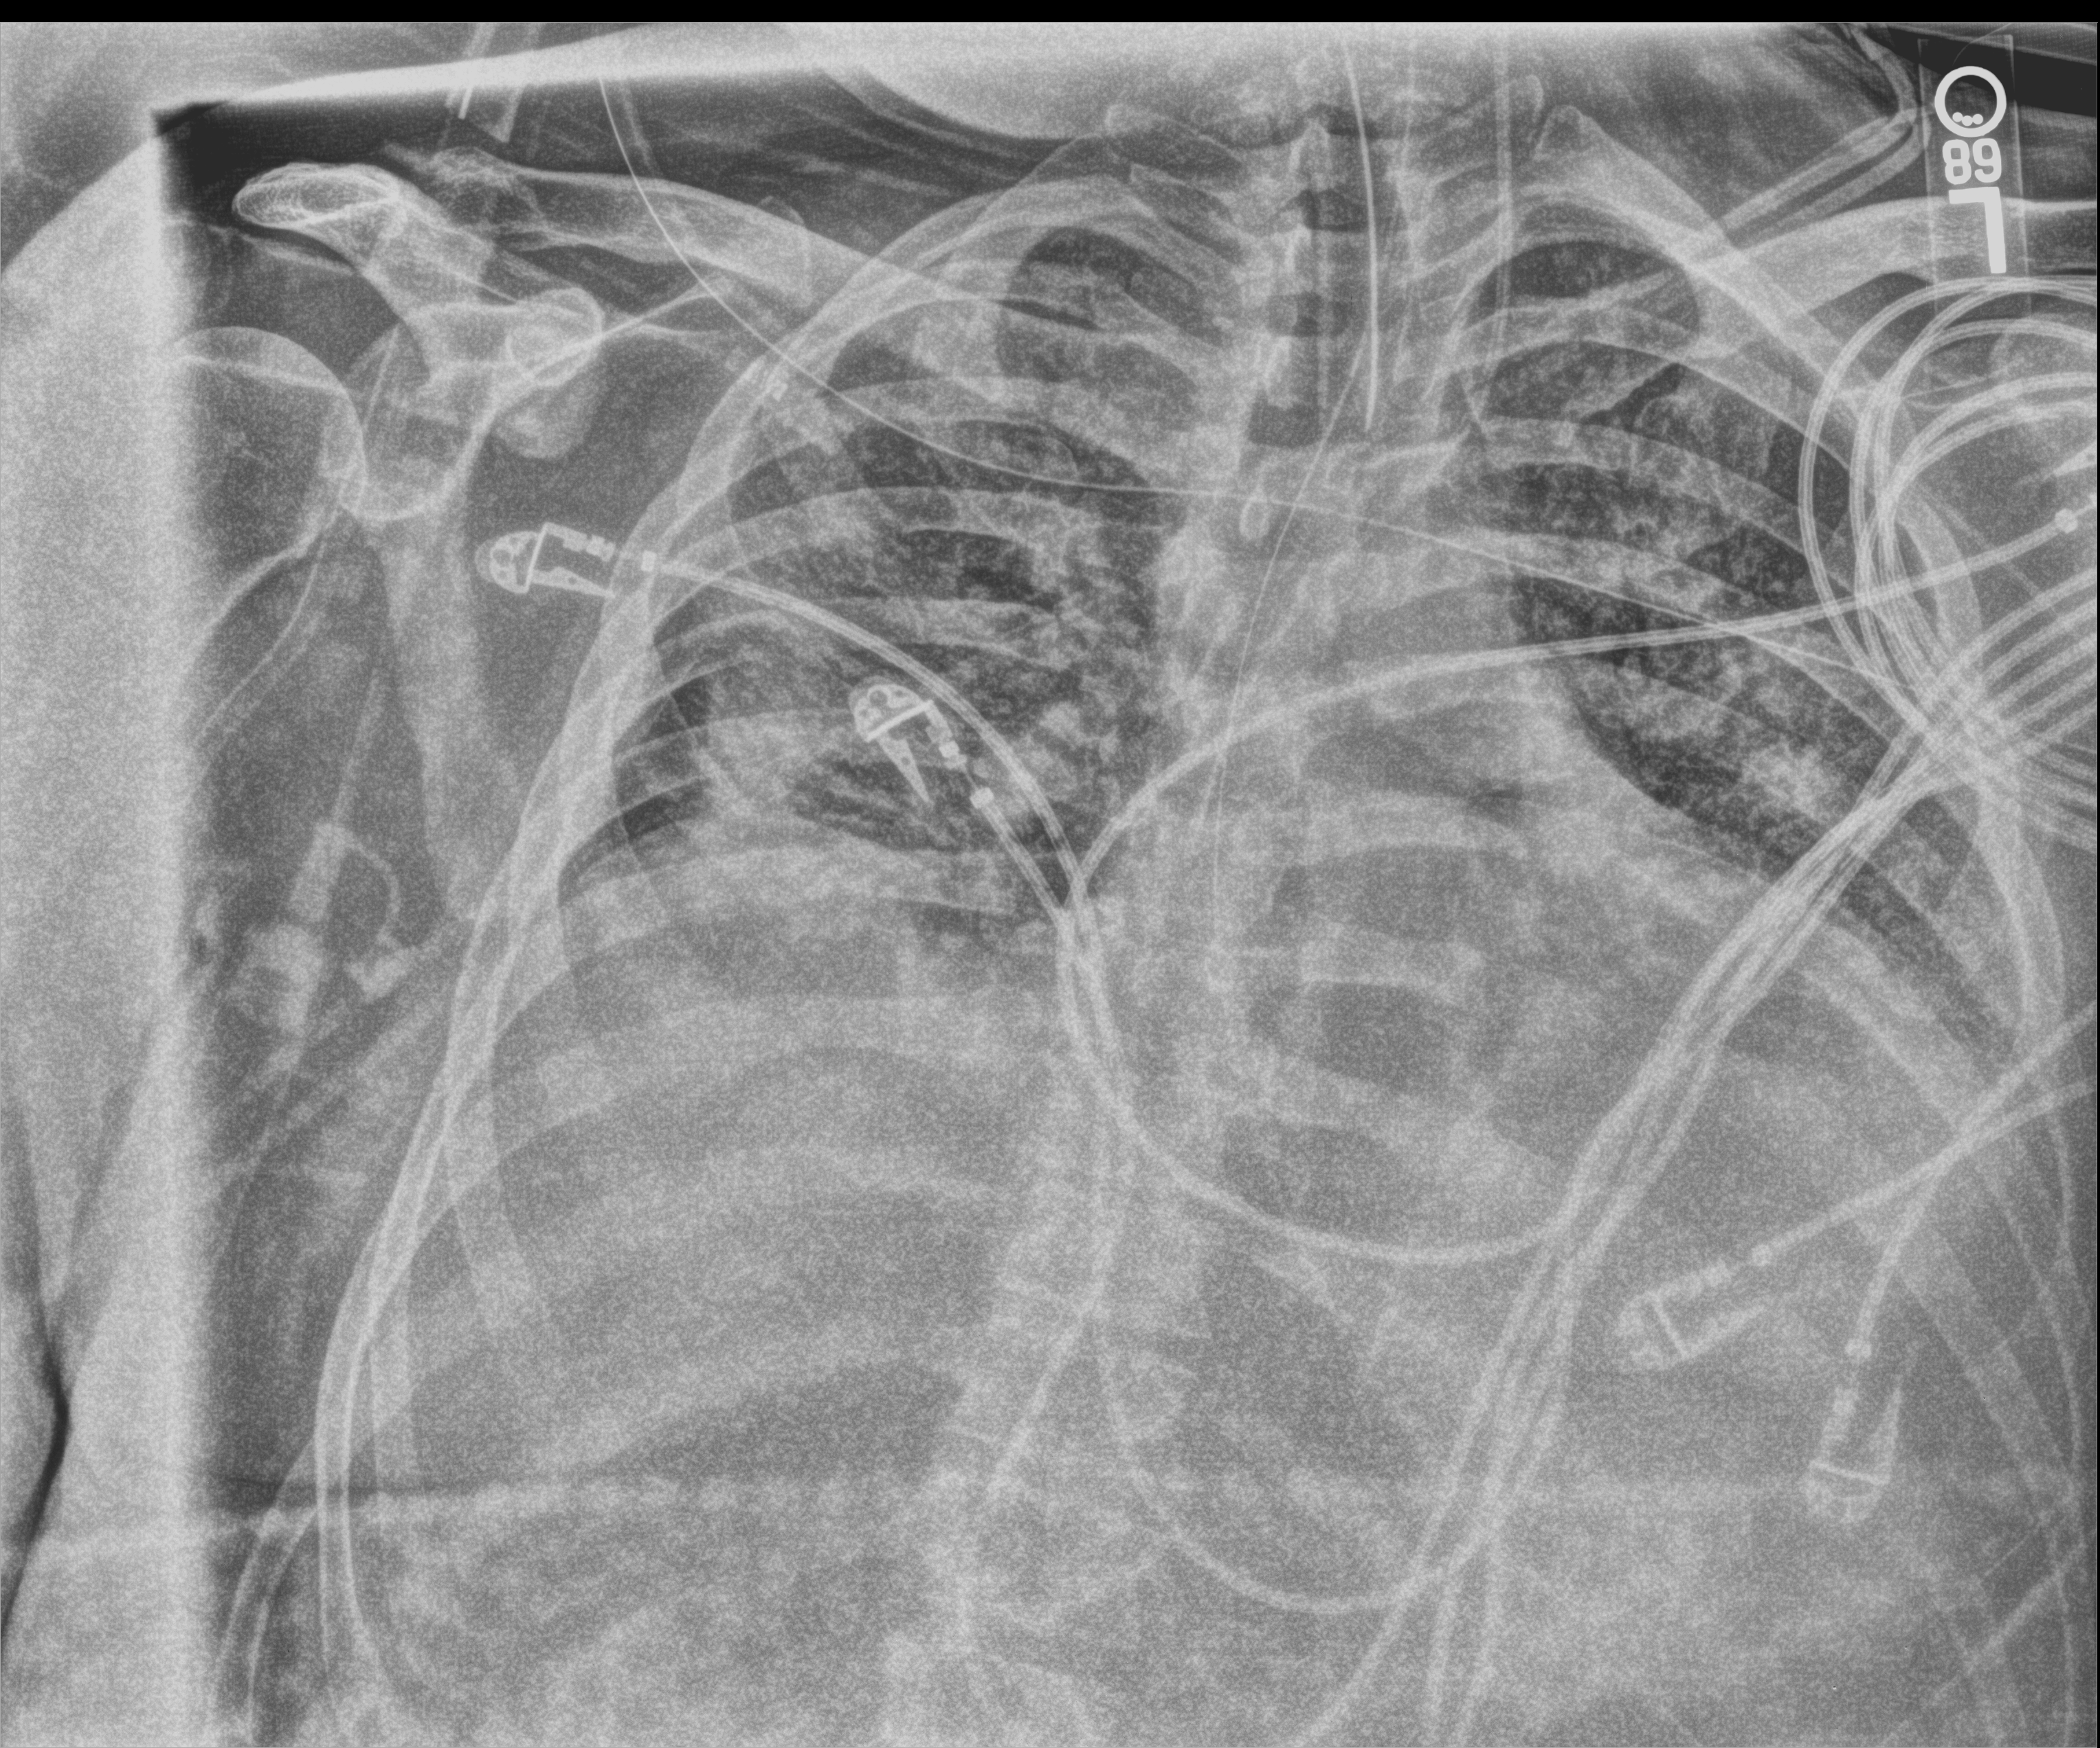
Bedside chest radiograph (computed radiography), anteroposterior (AP) projection. Male patient hospitalised with COVID-19, age 18–59 years.
Admission-level facts for this patient (not findings on this image; timing relative to this image not recorded):
- diabetes (admission record): no
- hypertension (admission record): yes
- mechanically ventilated during this hospital stay: yes